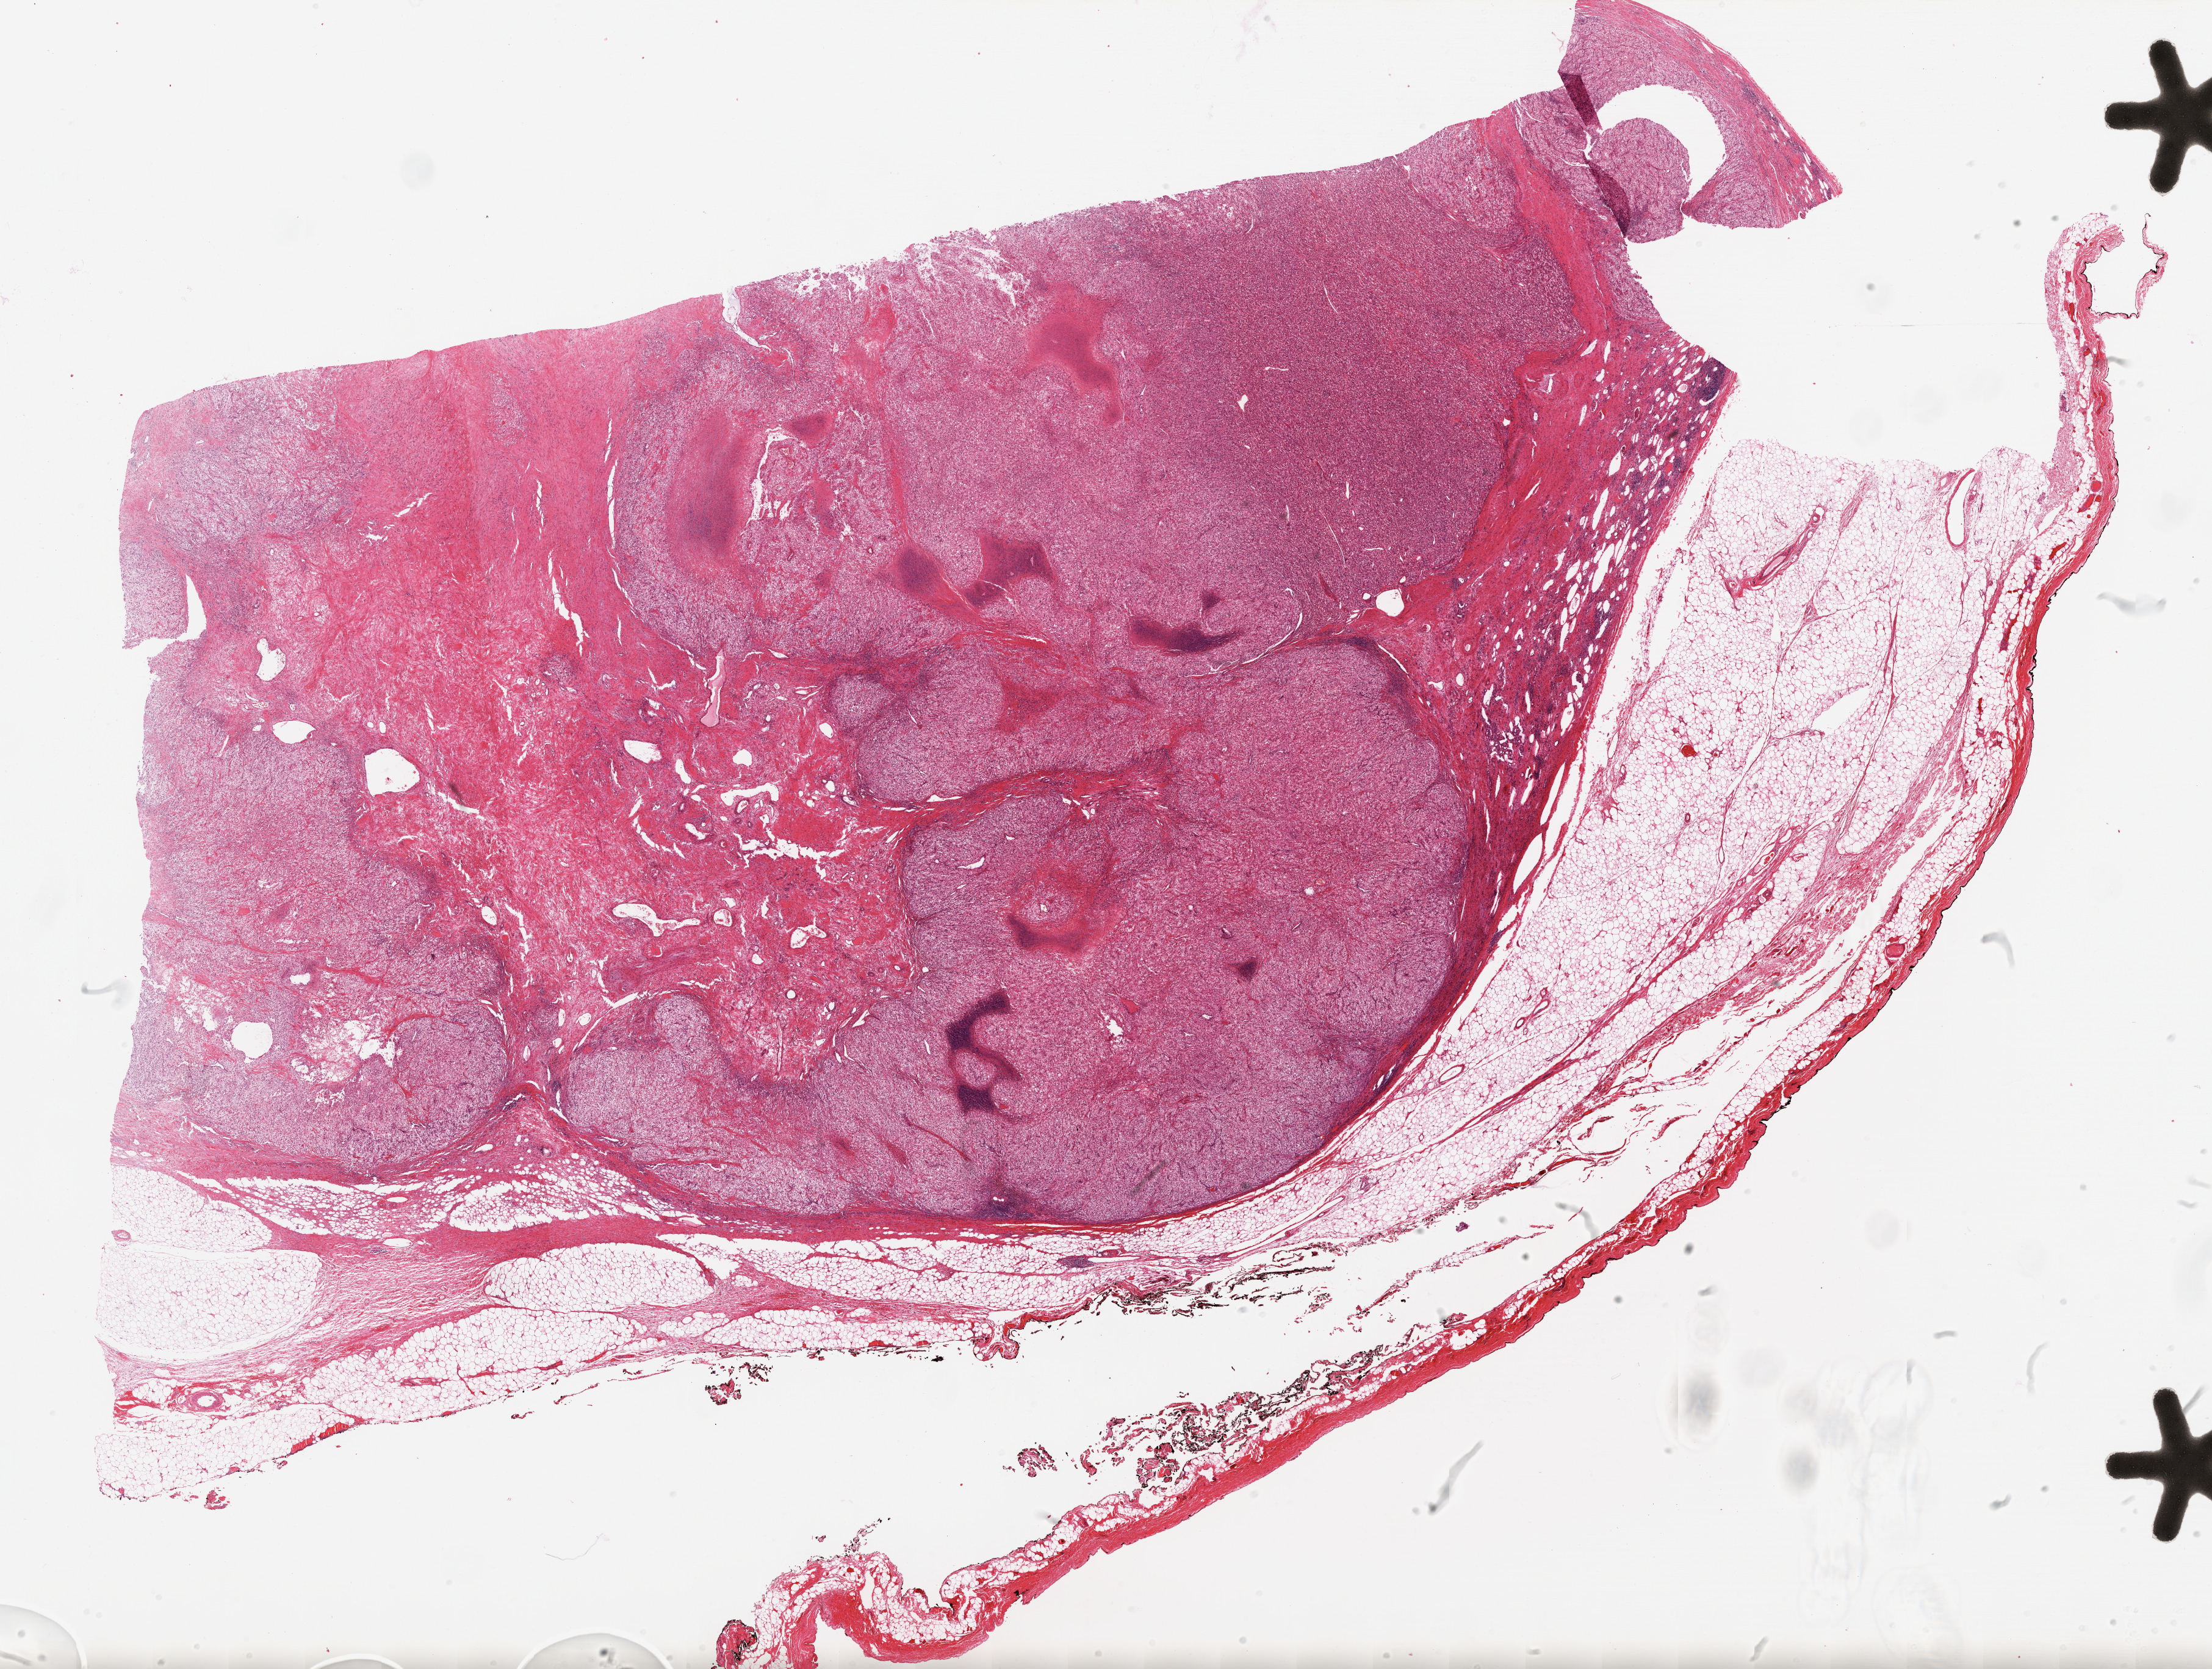
Digitized Hematoxylin and eosin (H&E) stained tissue section (whole slide), shown as a low-resolution overview of the whole scanned area (about 29.1 x 21.9 mm). Formalin-fixed paraffin-embedded (FFPE) diagnostic section. Kidney, primary tumour sample. Male, age 56 years at initial diagnosis. Histologic grade: G3 (poorly differentiated).
AJCC pathologic stage: IV. Diagnosis: Clear cell adenocarcinoma, NOS.